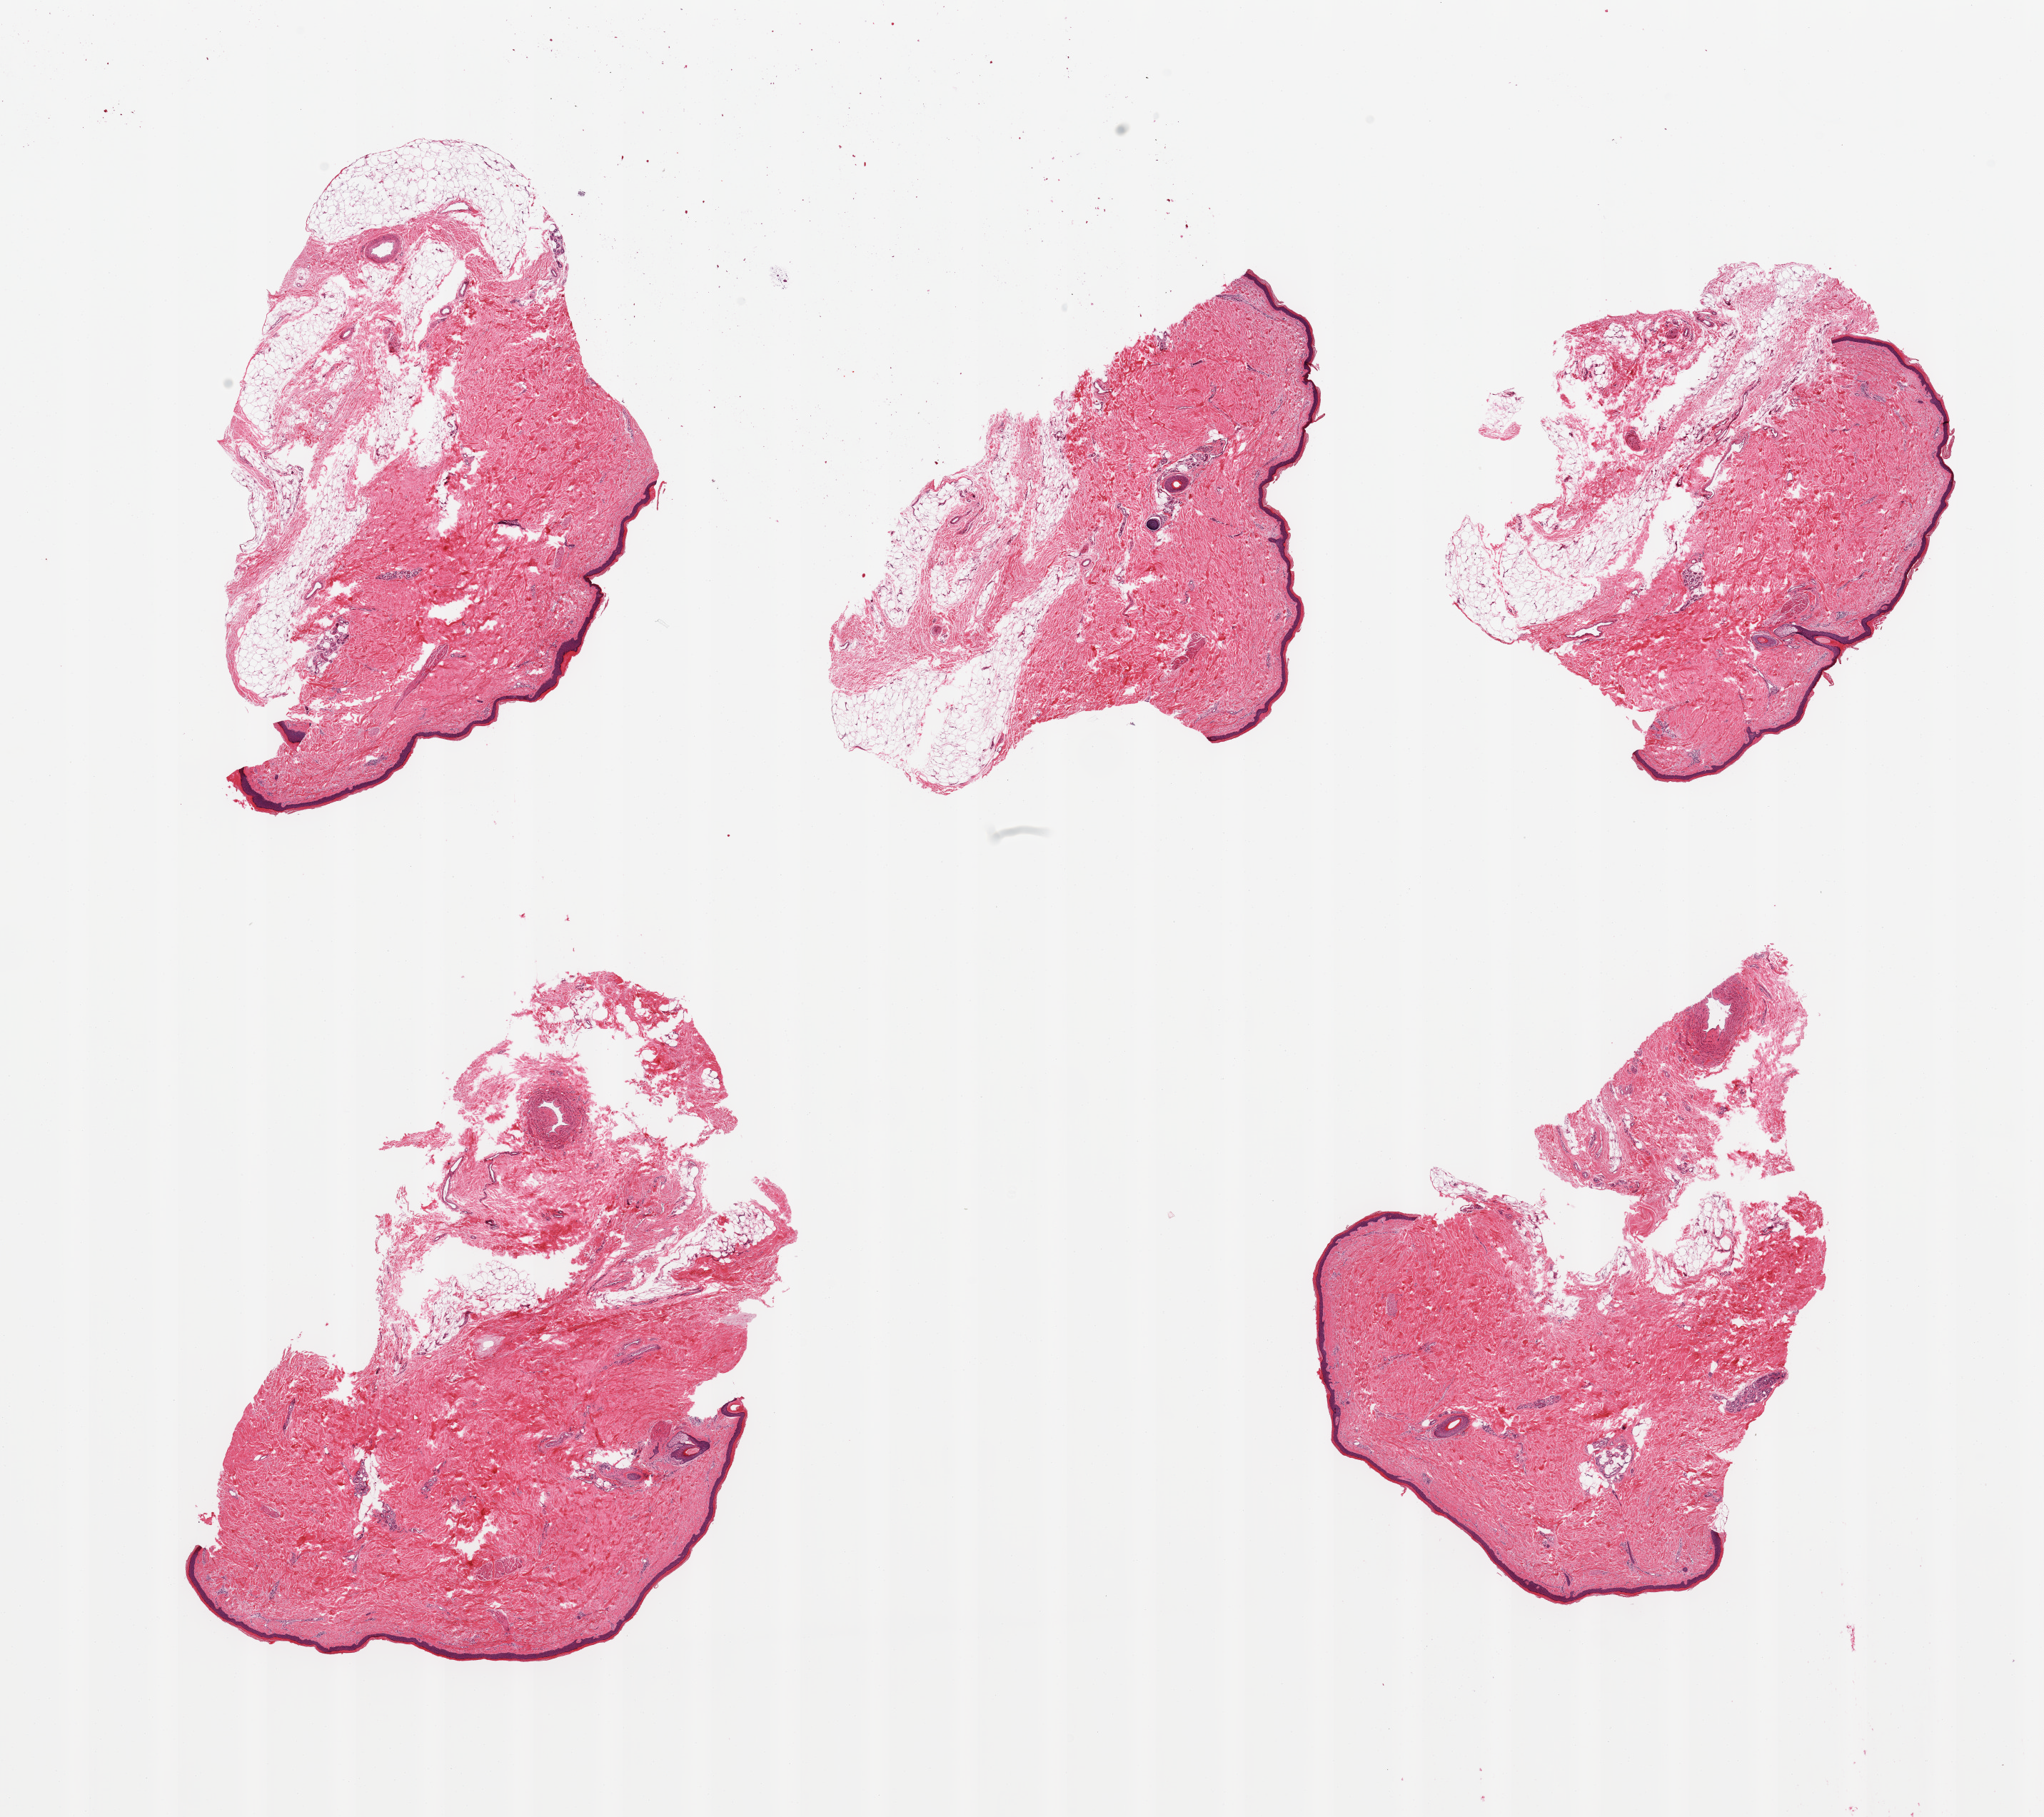
Whole-slide image, haematoxylin and eosin stain, brightfield, shown as a low-resolution overview of the whole scanned area (about 22.6 x 20.1 mm); PAXgene-fixed paraffin-embedded (PFPE) section; sampled site (target tissue): skin of lower leg; tissue donor sample. Donor: male.
* pathologist's review note for this sample: 5 pieces; poorly trimmed: up to 2mm subcutaneous fat present